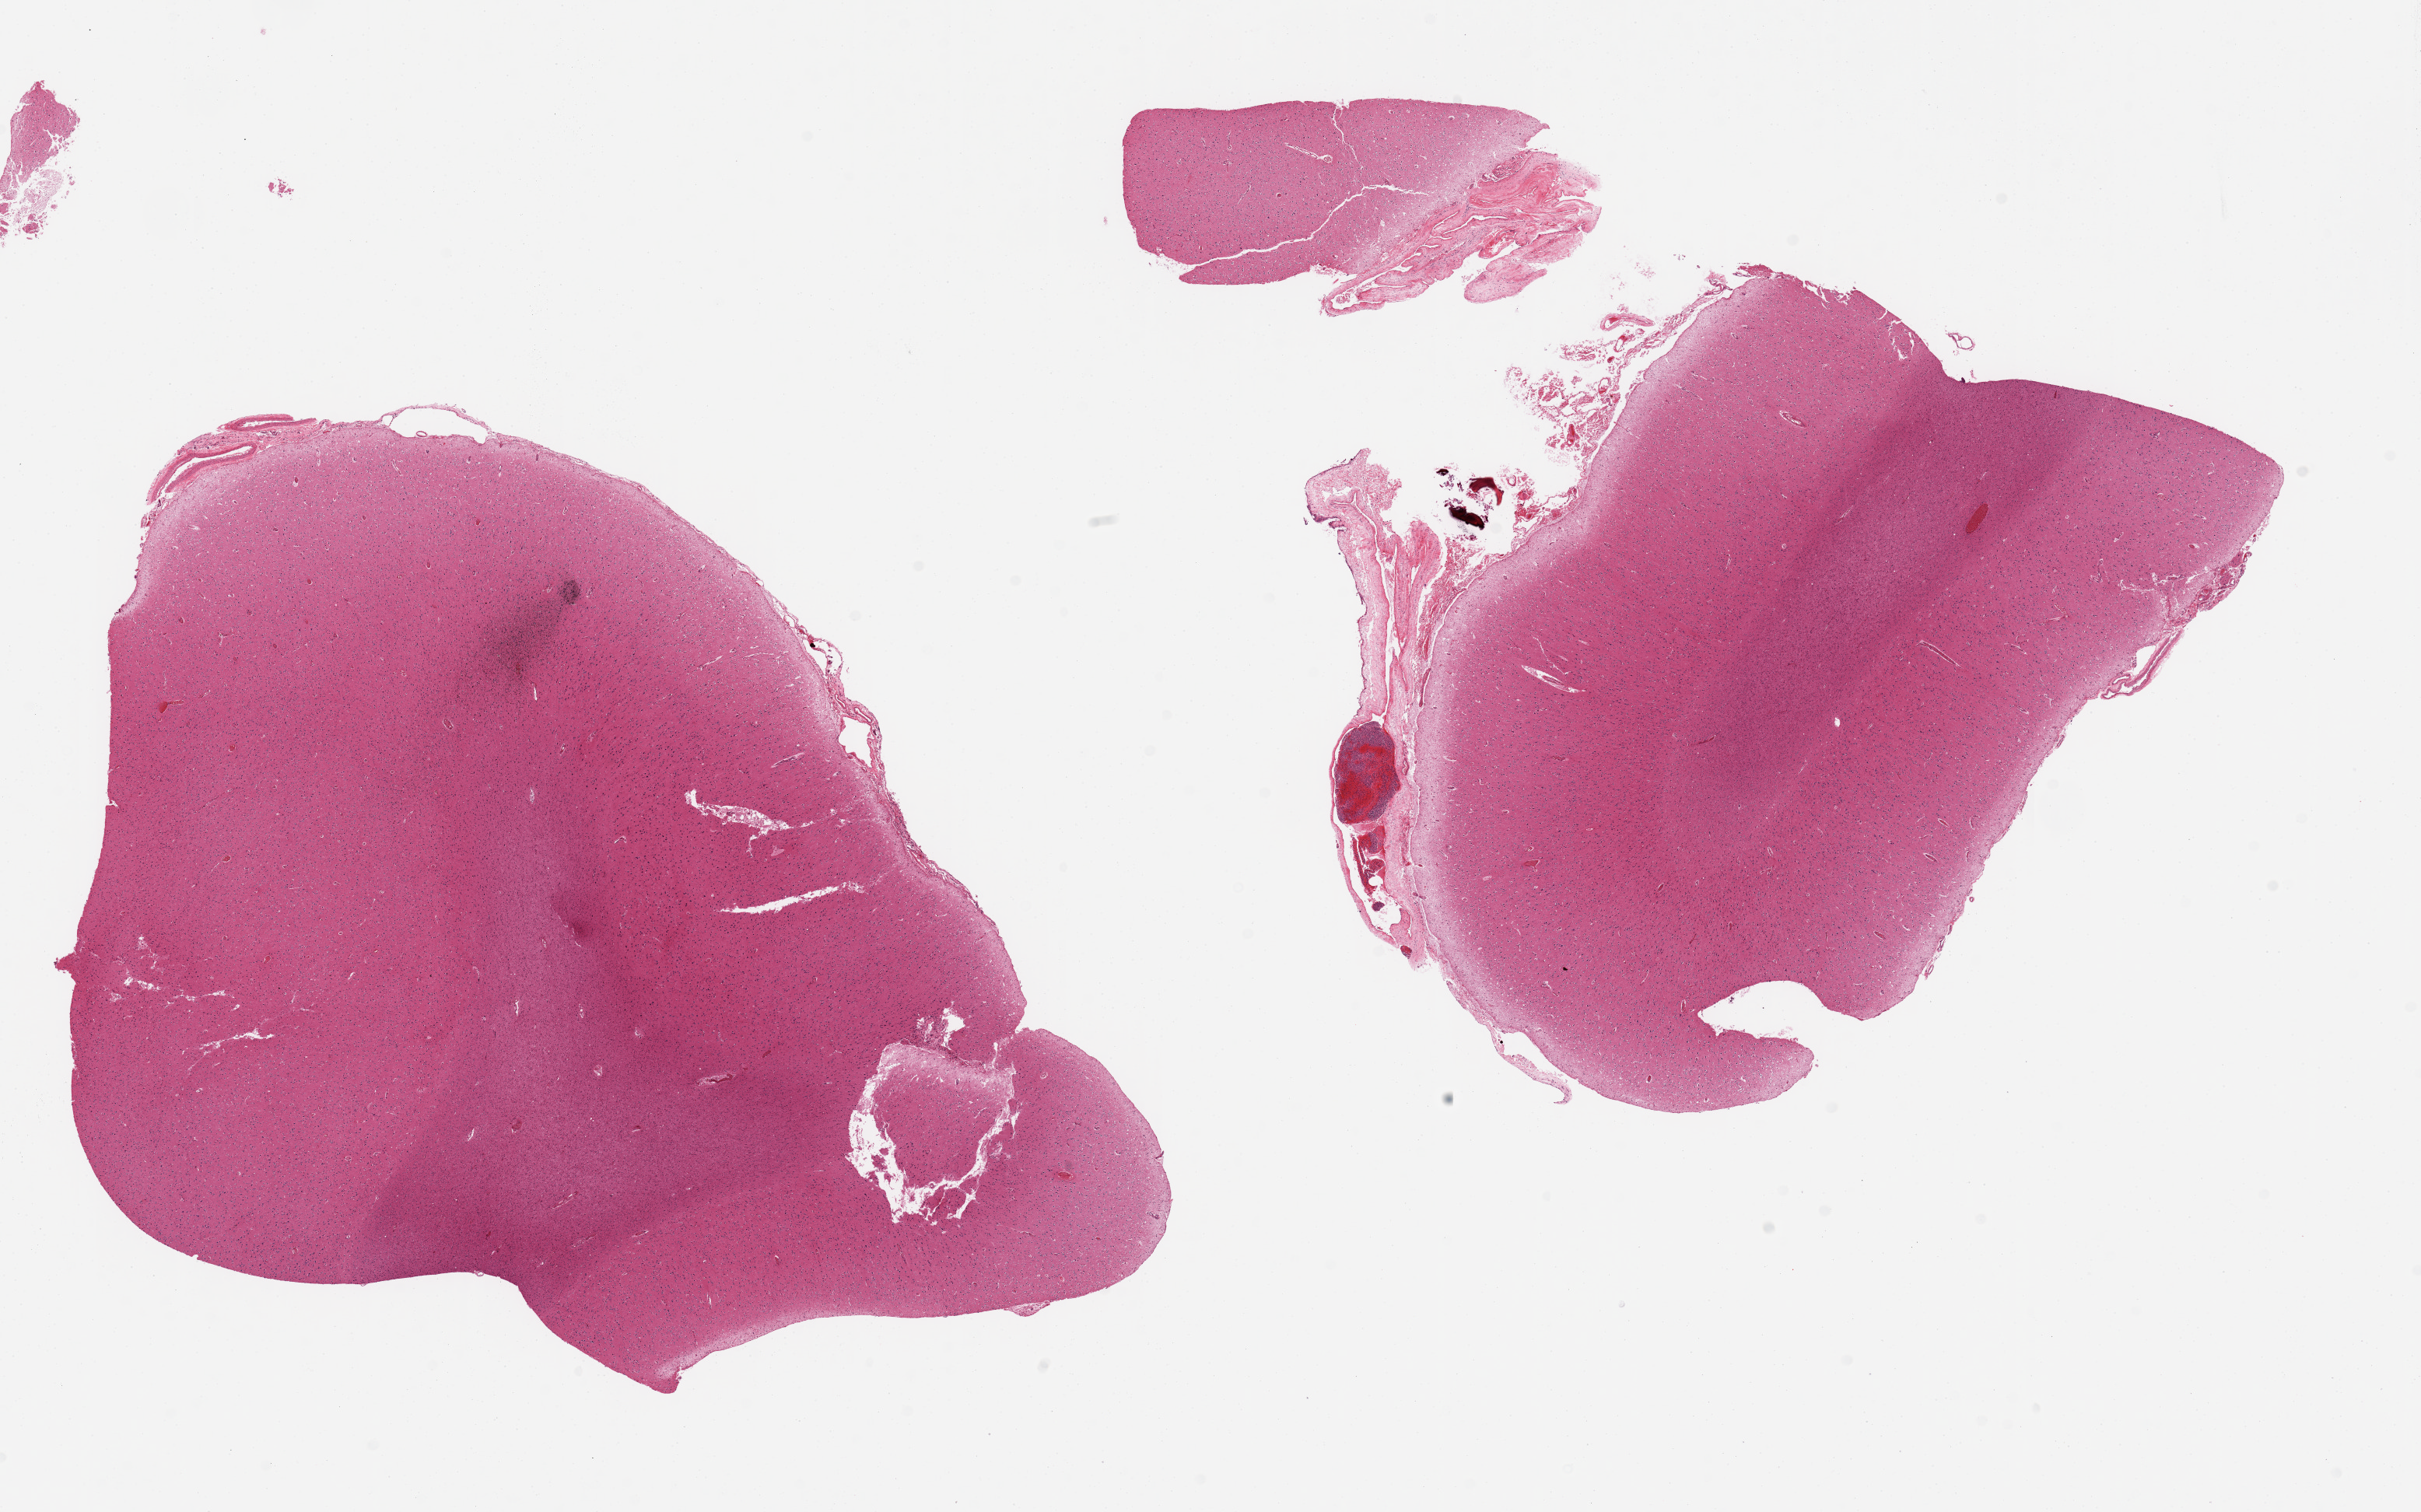
Haematoxylin and eosin whole-slide image, brightfield, low-resolution overview of the scanned area, about 24.6 x 15.4 mm (slide scanned at 20x); PAXgene-fixed paraffin-embedded (PFPE) section; section of cerebral cortex (target tissue); donor tissue sample. Donor sex: male.
* pathologist's review note for this sample: 2 pieces, ~5-10% adherent meninges